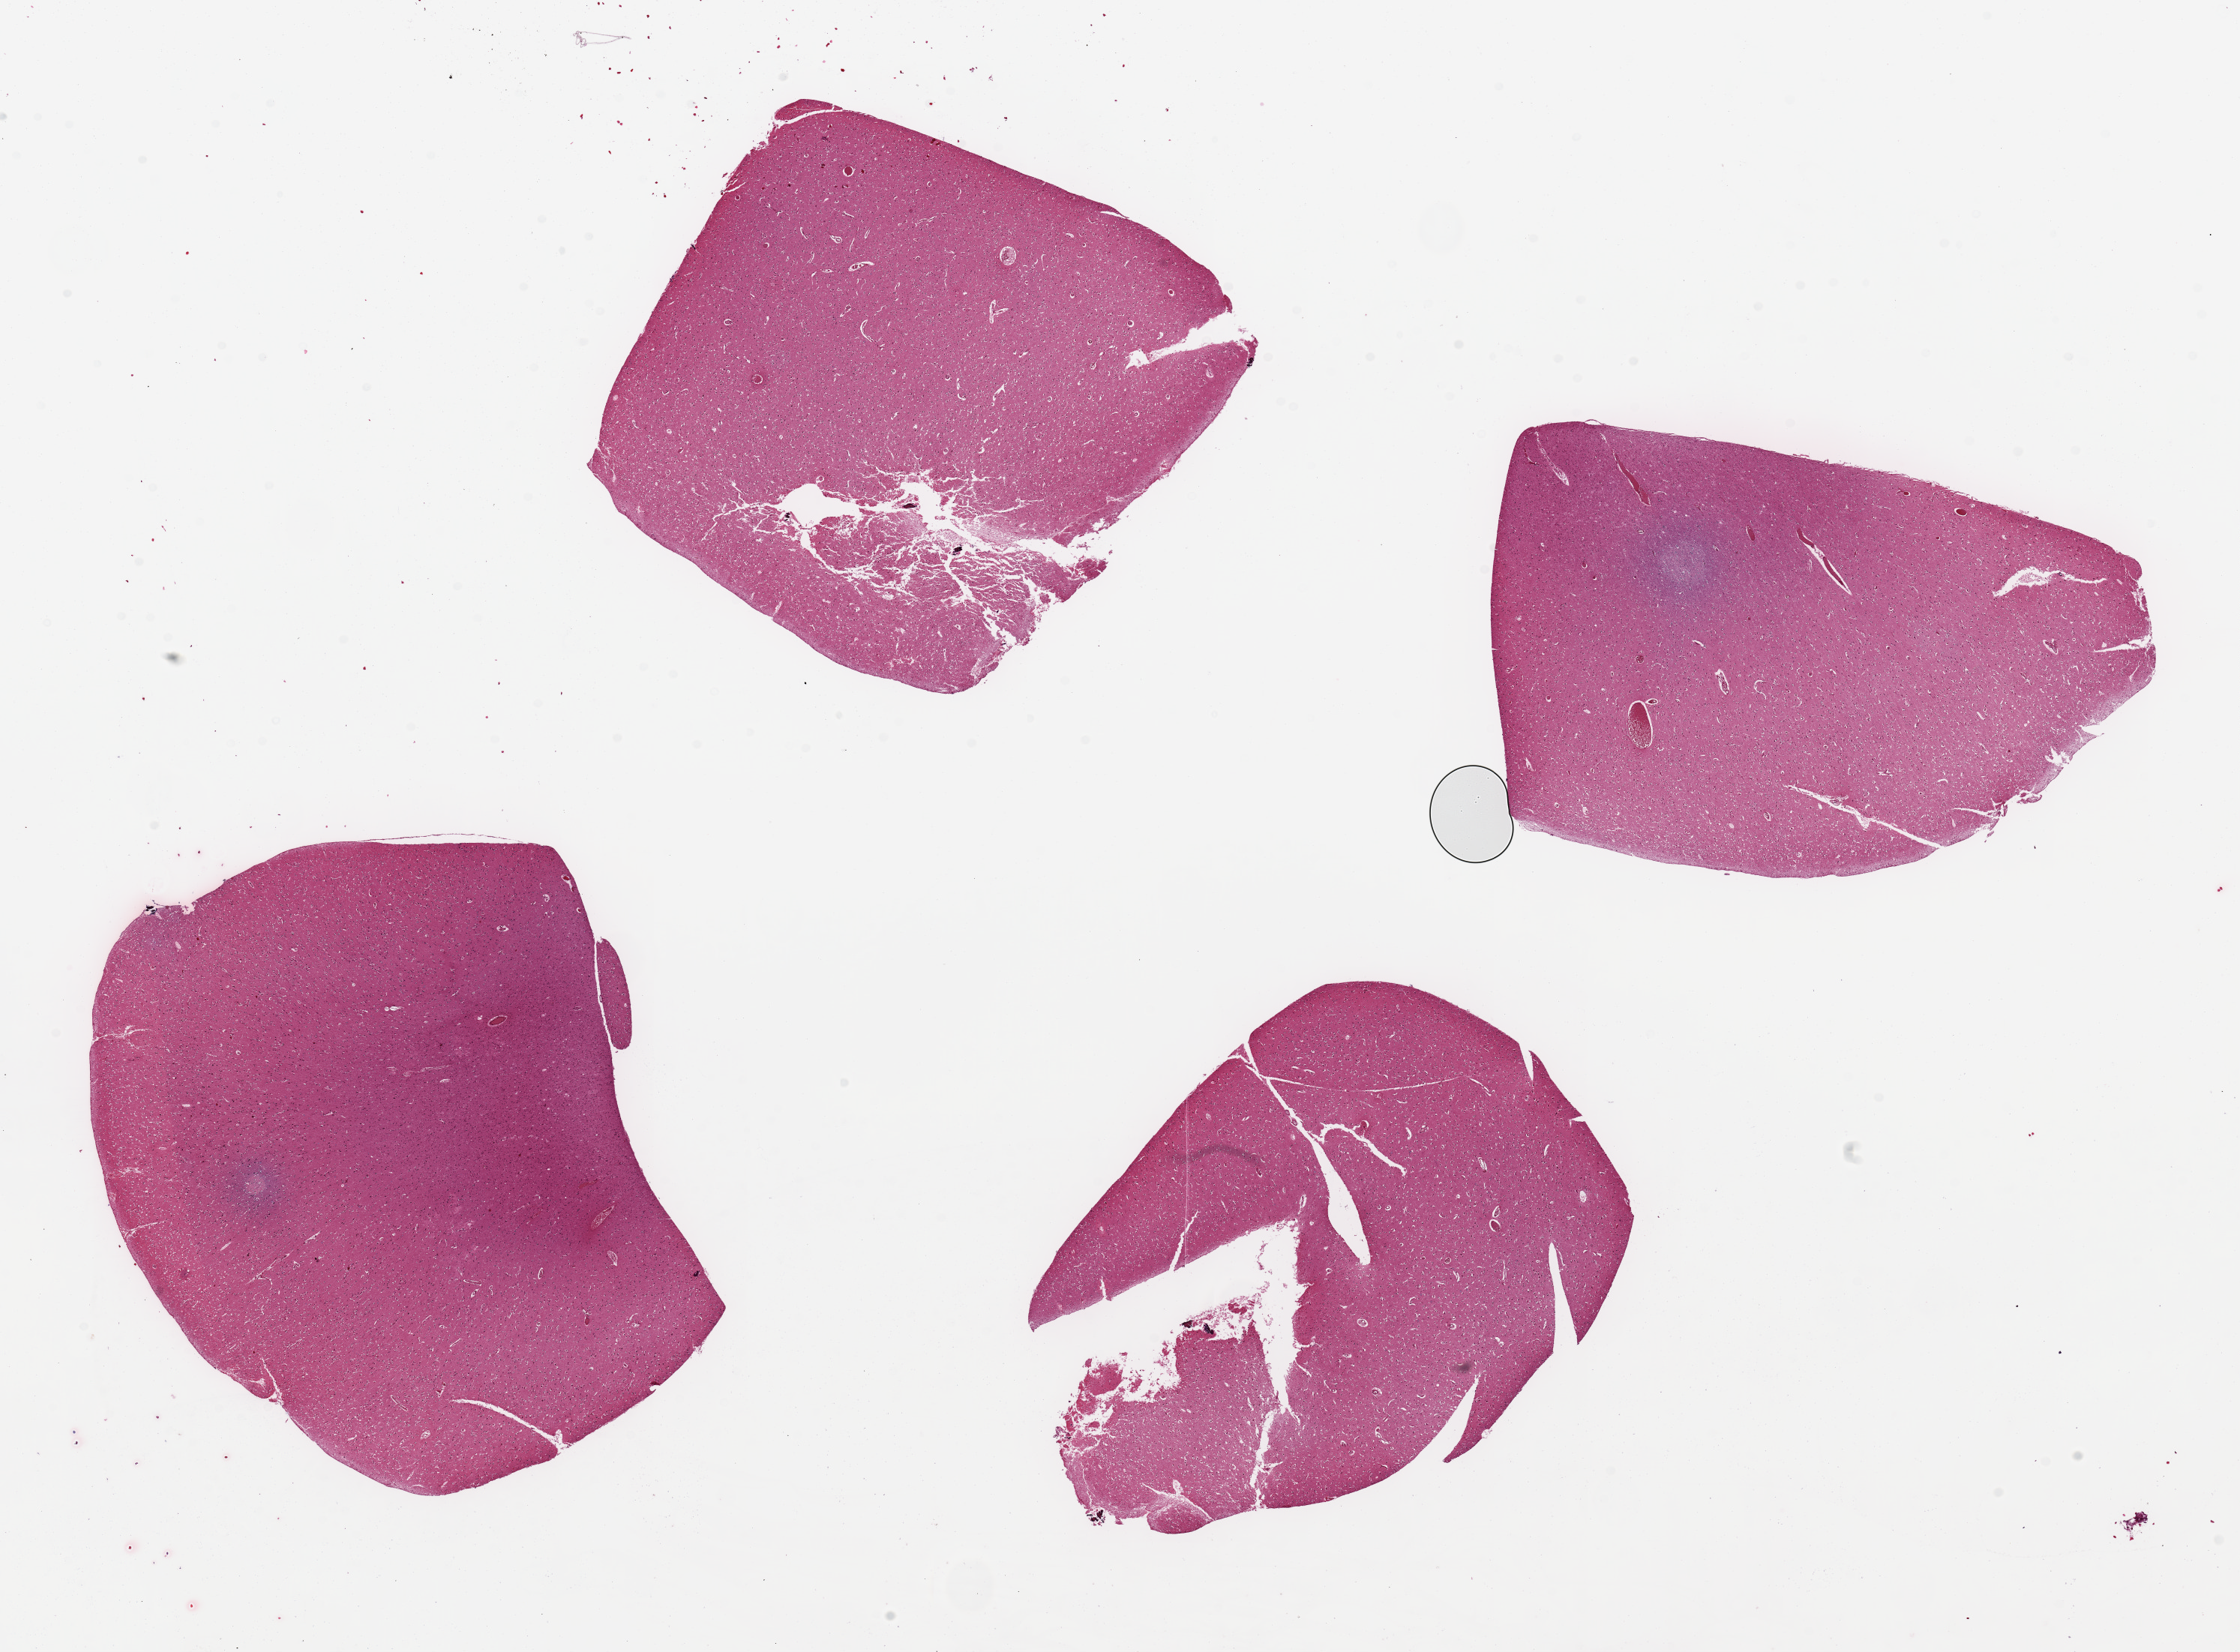
Hematoxylin and eosin (H&E) whole-slide image, brightfield, whole scanned area (about 23.6 x 17.4 mm) shown as a low-resolution overview, PAXgene-fixed, paraffin-embedded tissue, section of cerebral cortex (target tissue), donor tissue sample.
Review note (as recorded): 4 pieces up to 6x5 mm; two pieces with focal artifacts and bone fragments.